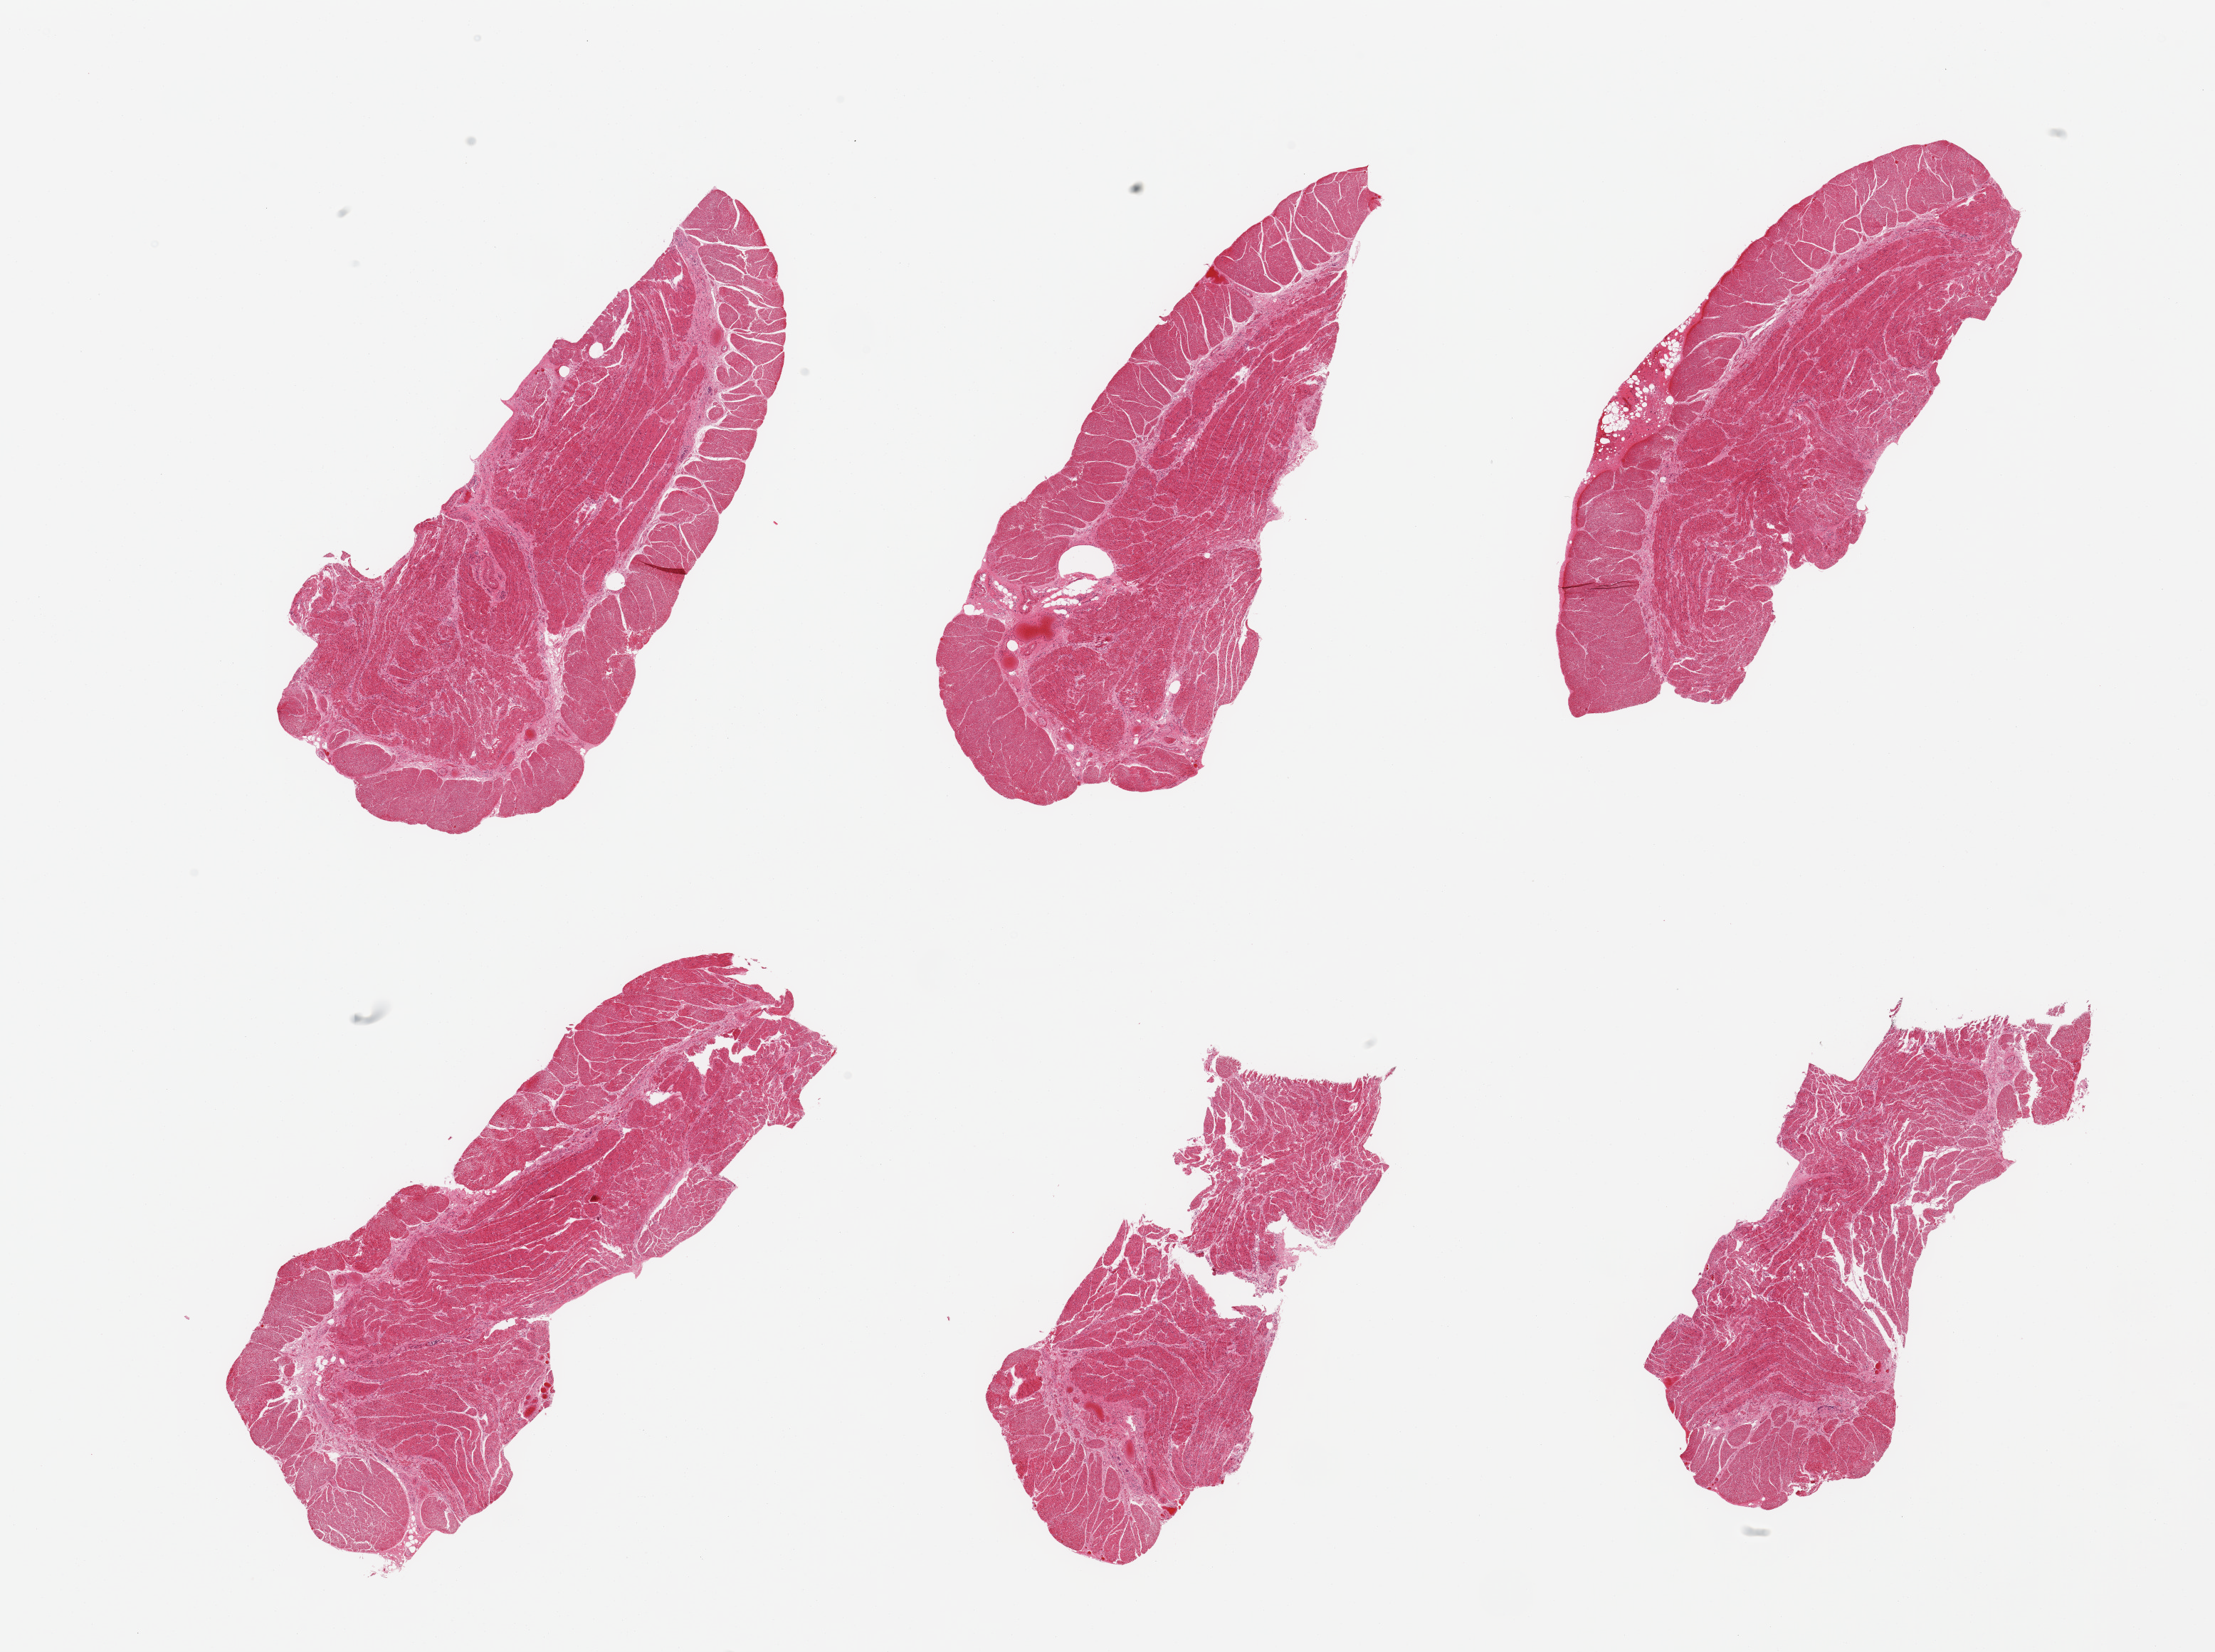
Whole-slide image, hematoxylin and eosin (H&E) stain, low-resolution overview of the scanned area, about 24.6 x 18.4 mm (acquisition: 20x scan), PAXgene-fixed paraffin-embedded (PFPE) section, section of gastroesophageal junction (target tissue), donor tissue sample. Donor: male.
* reviewer comment on this tissue sample: 6 piece, confirmed target muscularis